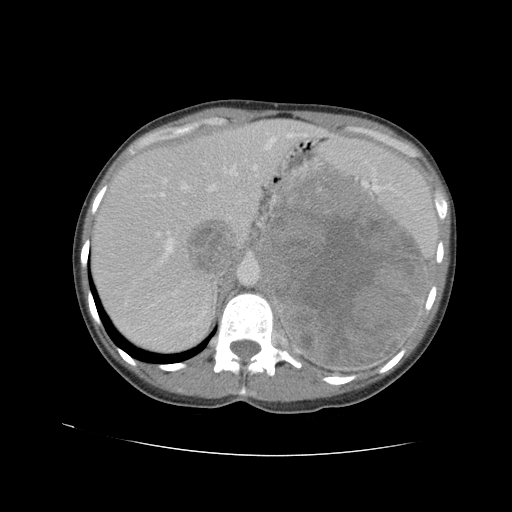
Contrast-enhanced abdominal CT, one axial slice. Slice 72 of 90 in the series (ordered by position). Intravenous contrast given. Soft-tissue window (W 400 / L 40 HU). 5 mm slice thickness. 512 × 512 image matrix, field of view 360 × 360 mm. Female patient. From the clinical record (not read from this slice): diagnosis: adrenocortical carcinoma; tumour side: left adrenal; tumour size at pathology: 18 cm; Ki-67 index: 11 %; stage (as recorded): 3.
Structures marked on this image (semi-automatically segmented with operator editing):
- mass: box from (x=258, y=166) to (x=425, y=367) px